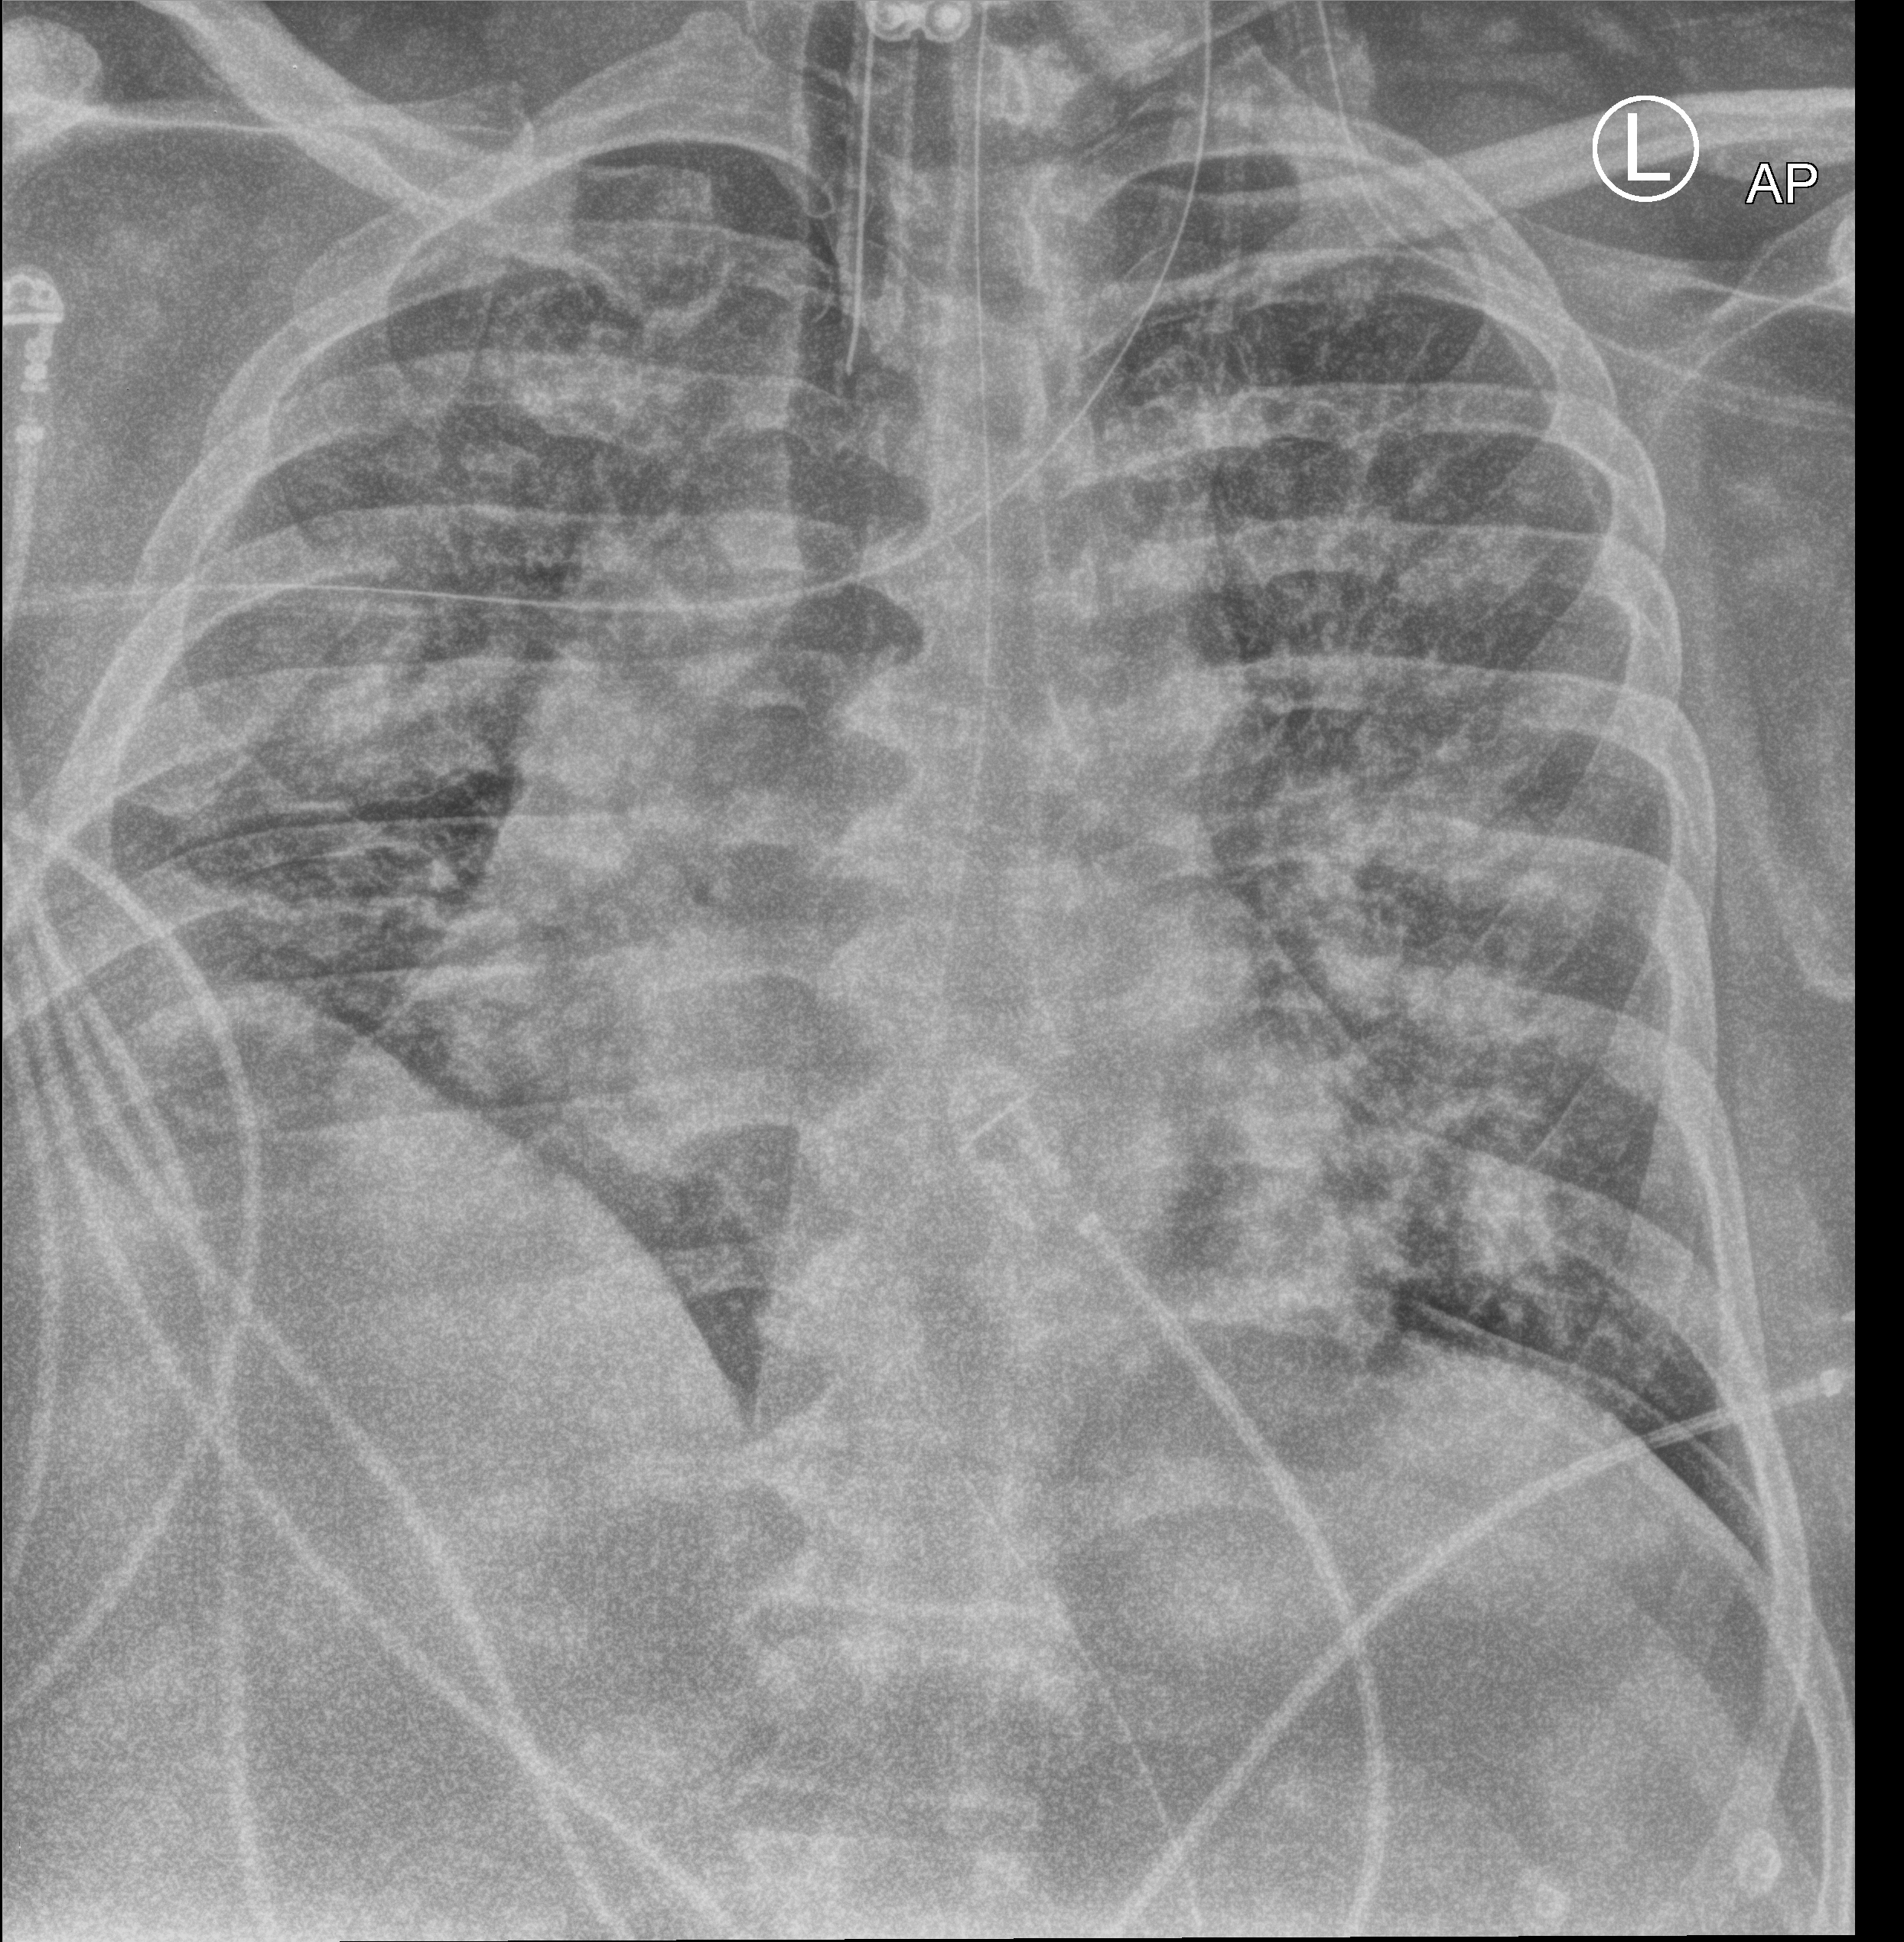
Bedside chest radiograph (computed radiography). Patient hospitalised with COVID-19; male, aged 18–59 years.
From the hospital-stay record, not from the radiograph (when in the stay this image was taken is not recorded): smoking status (admission record): never; length of hospital stay: 47 days; diabetes (admission record): no.